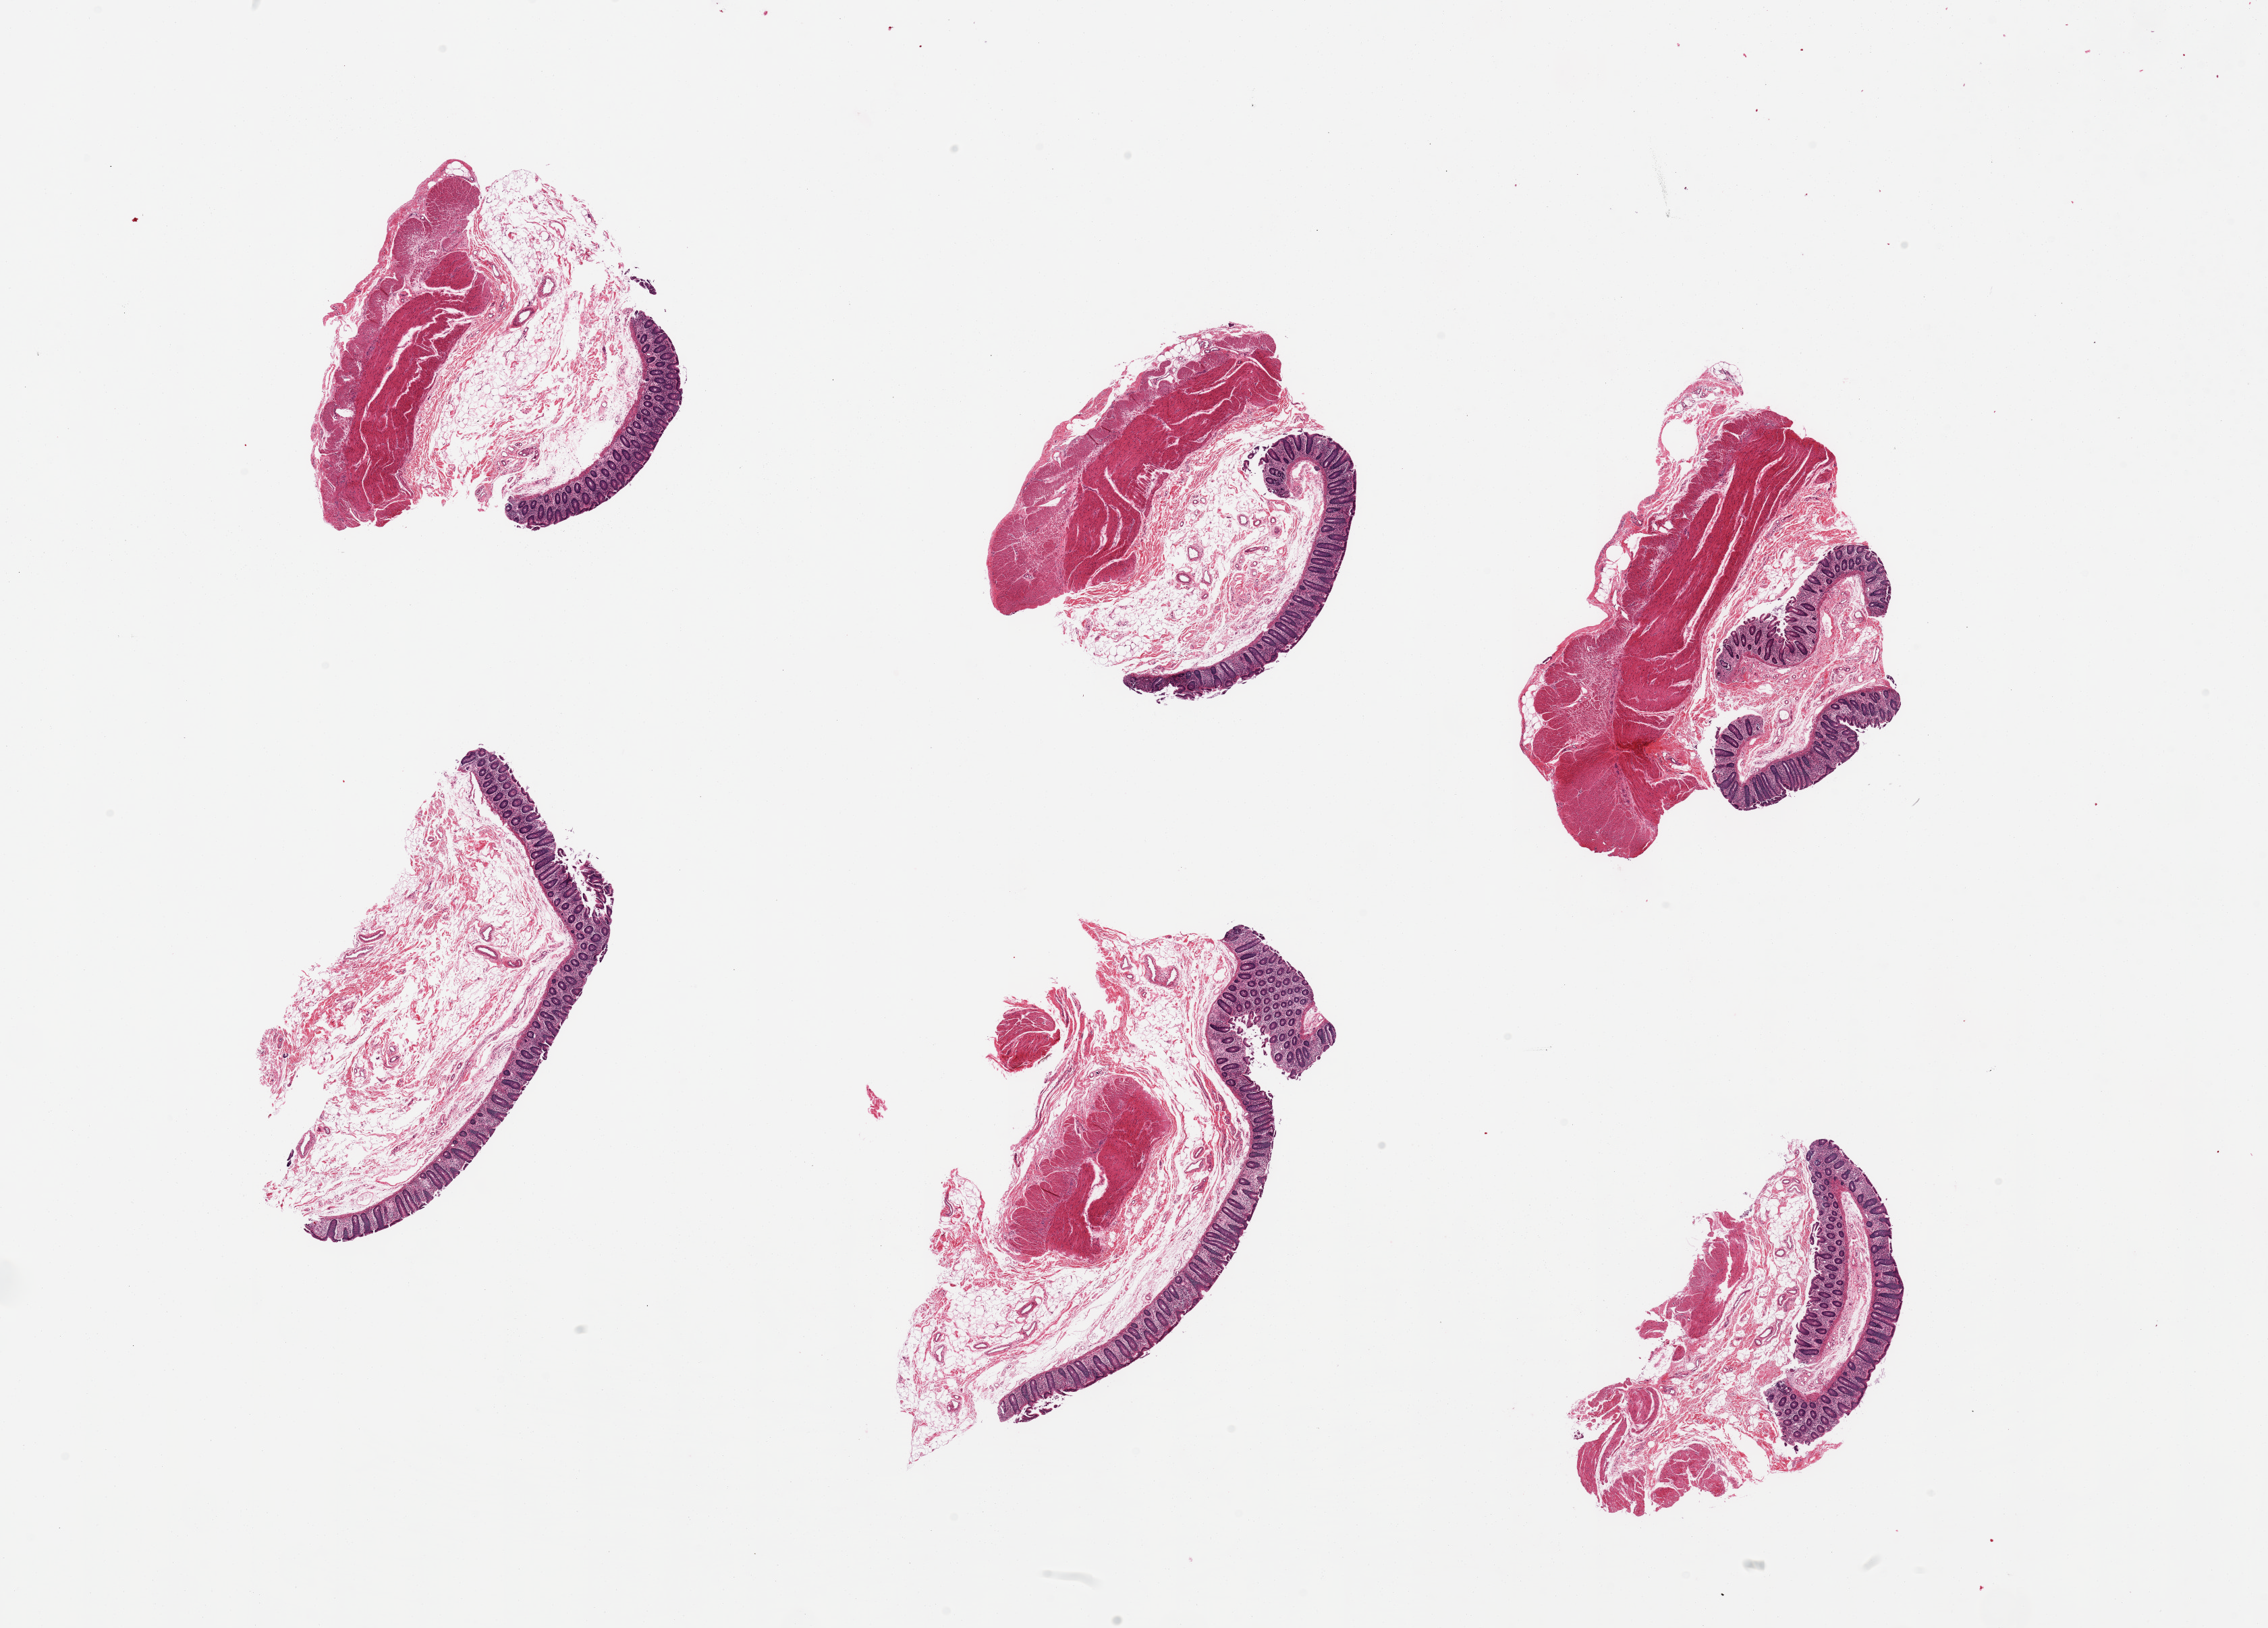
Whole-slide image, haematoxylin and eosin stain — low-resolution overview of the scanned area, about 26.6 x 19.1 mm; PAXgene-fixed paraffin-embedded (PFPE) section; target tissue: transverse colon; tissue donor sample.
* reviewer comment on this tissue sample: 6 pieces